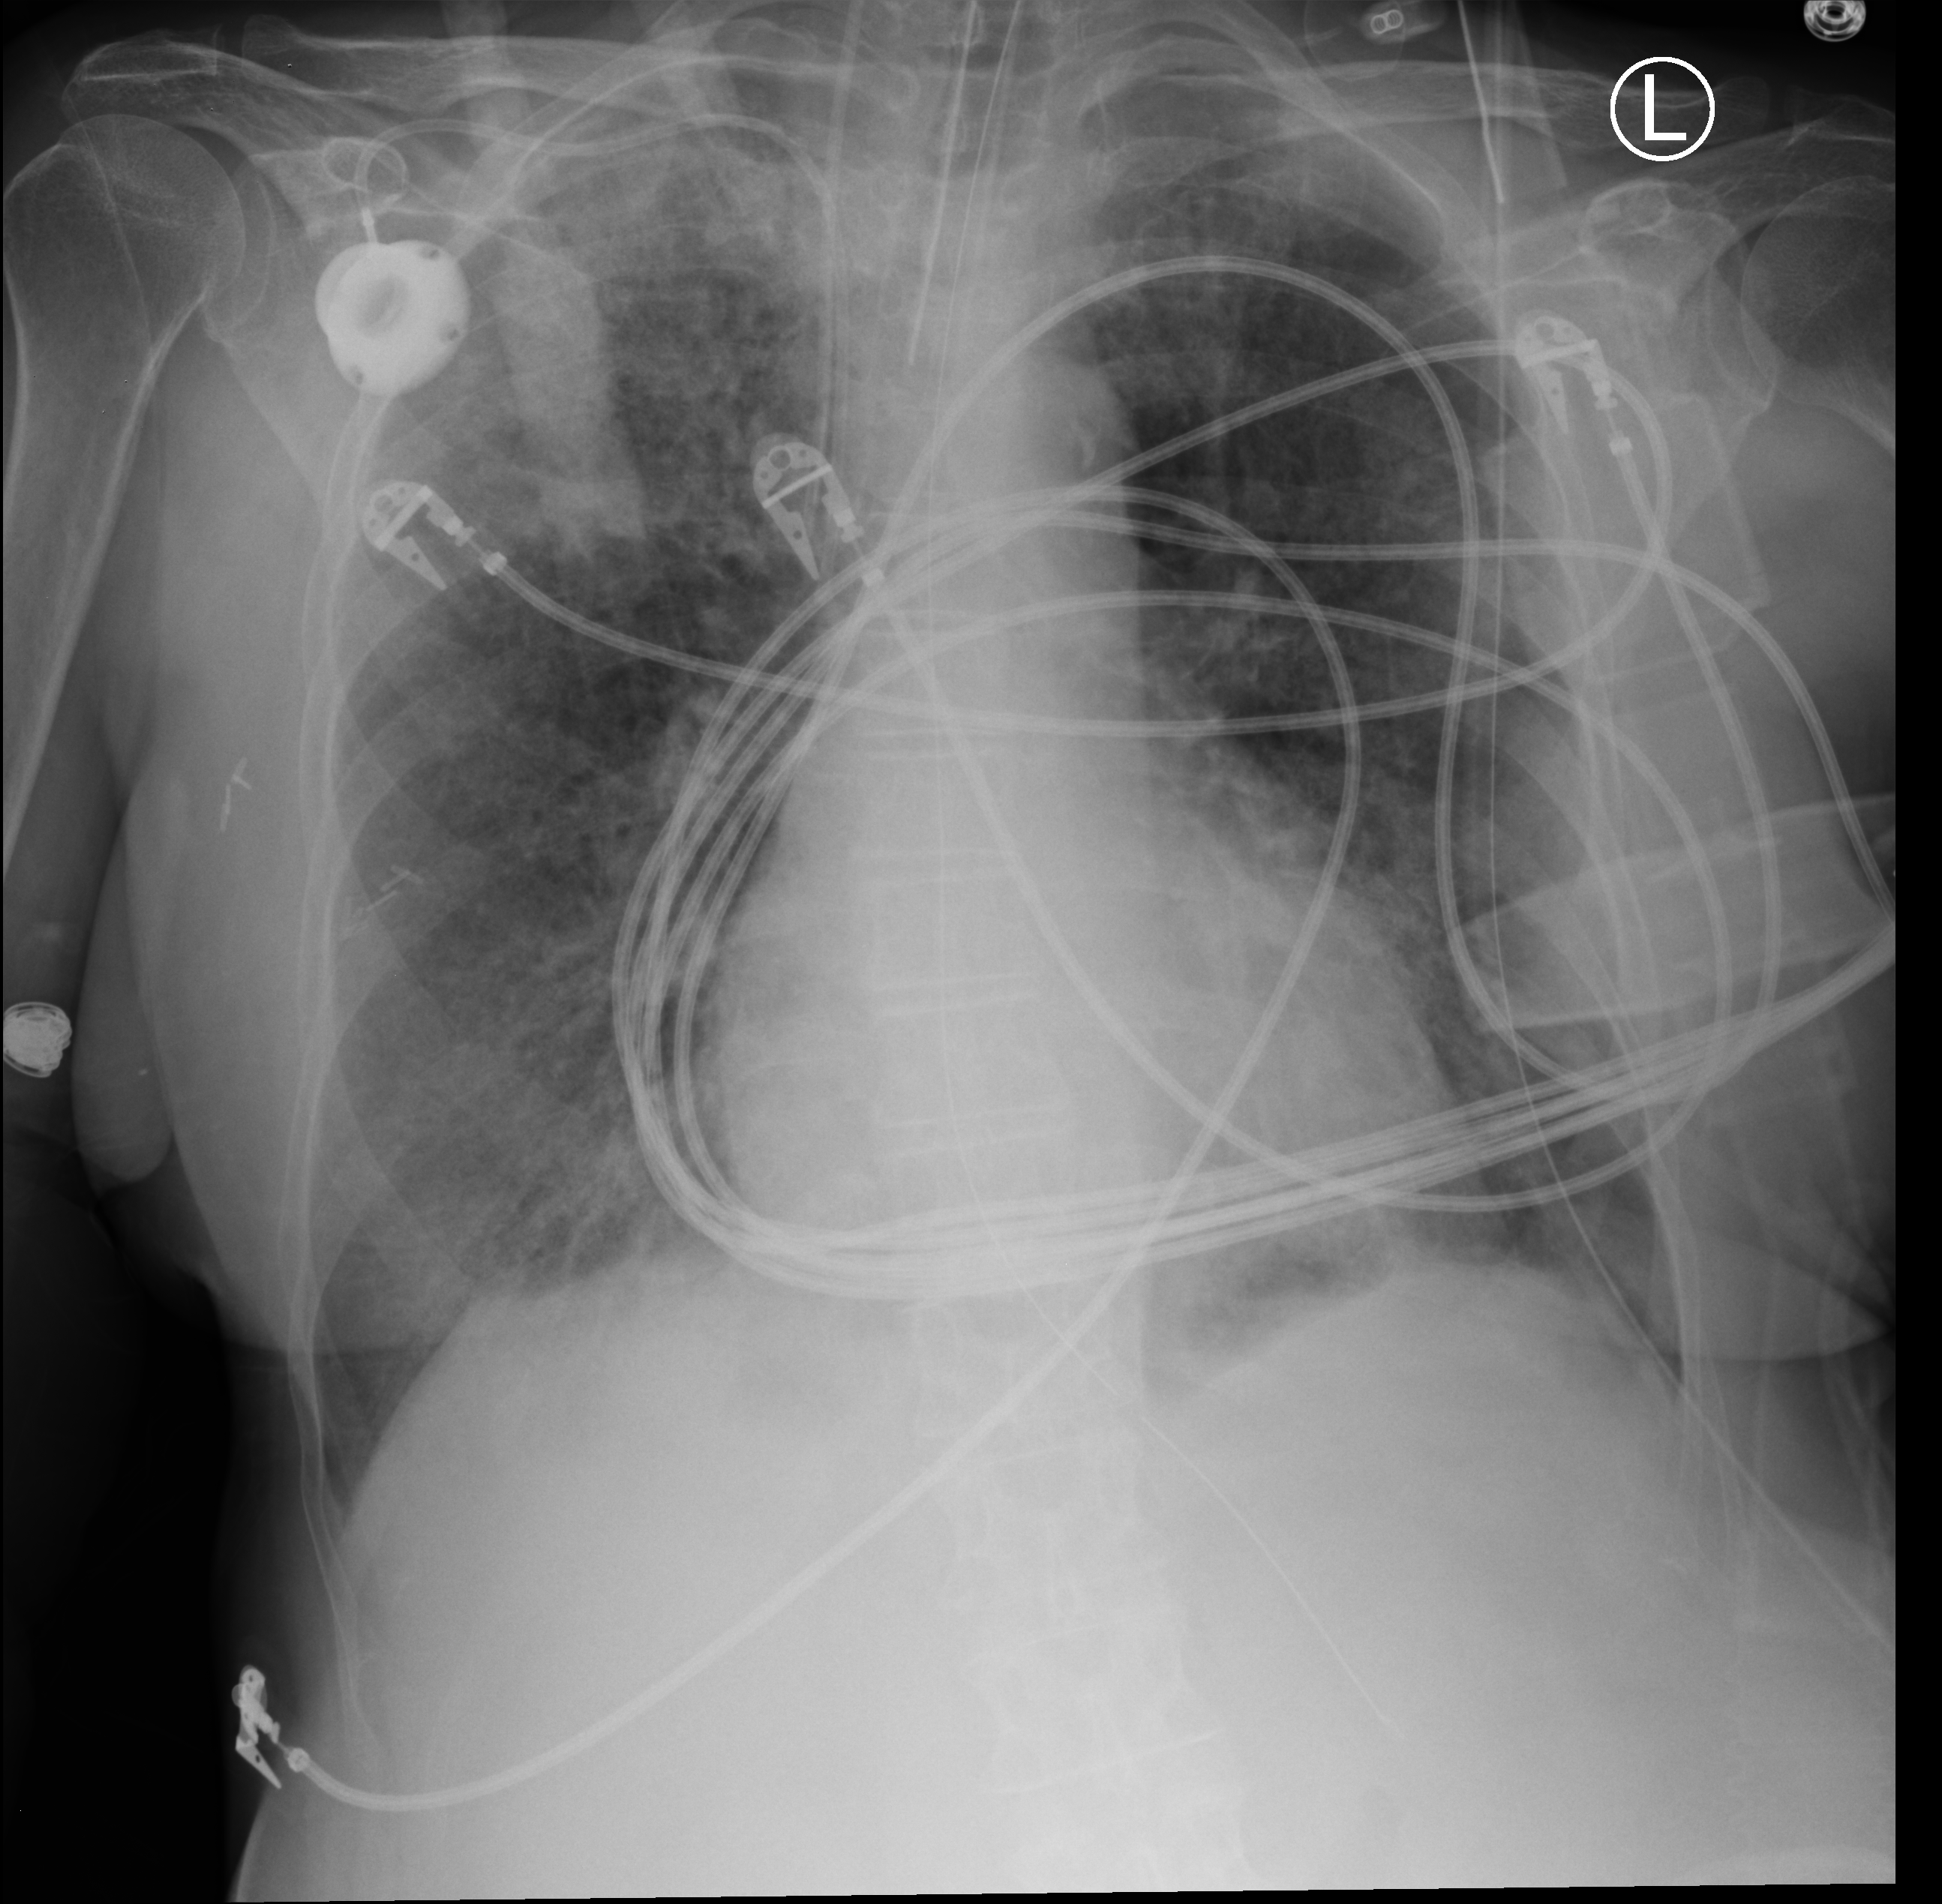
Portable chest radiograph, anteroposterior (AP) projection. Female patient hospitalised with COVID-19, age 60–74 years.
Admission-level facts for this patient (not findings on this image; timing relative to this image not recorded): mechanically ventilated during this hospital stay: yes; hypertension (admission record): yes; admitted to intensive care during this hospital stay: yes.